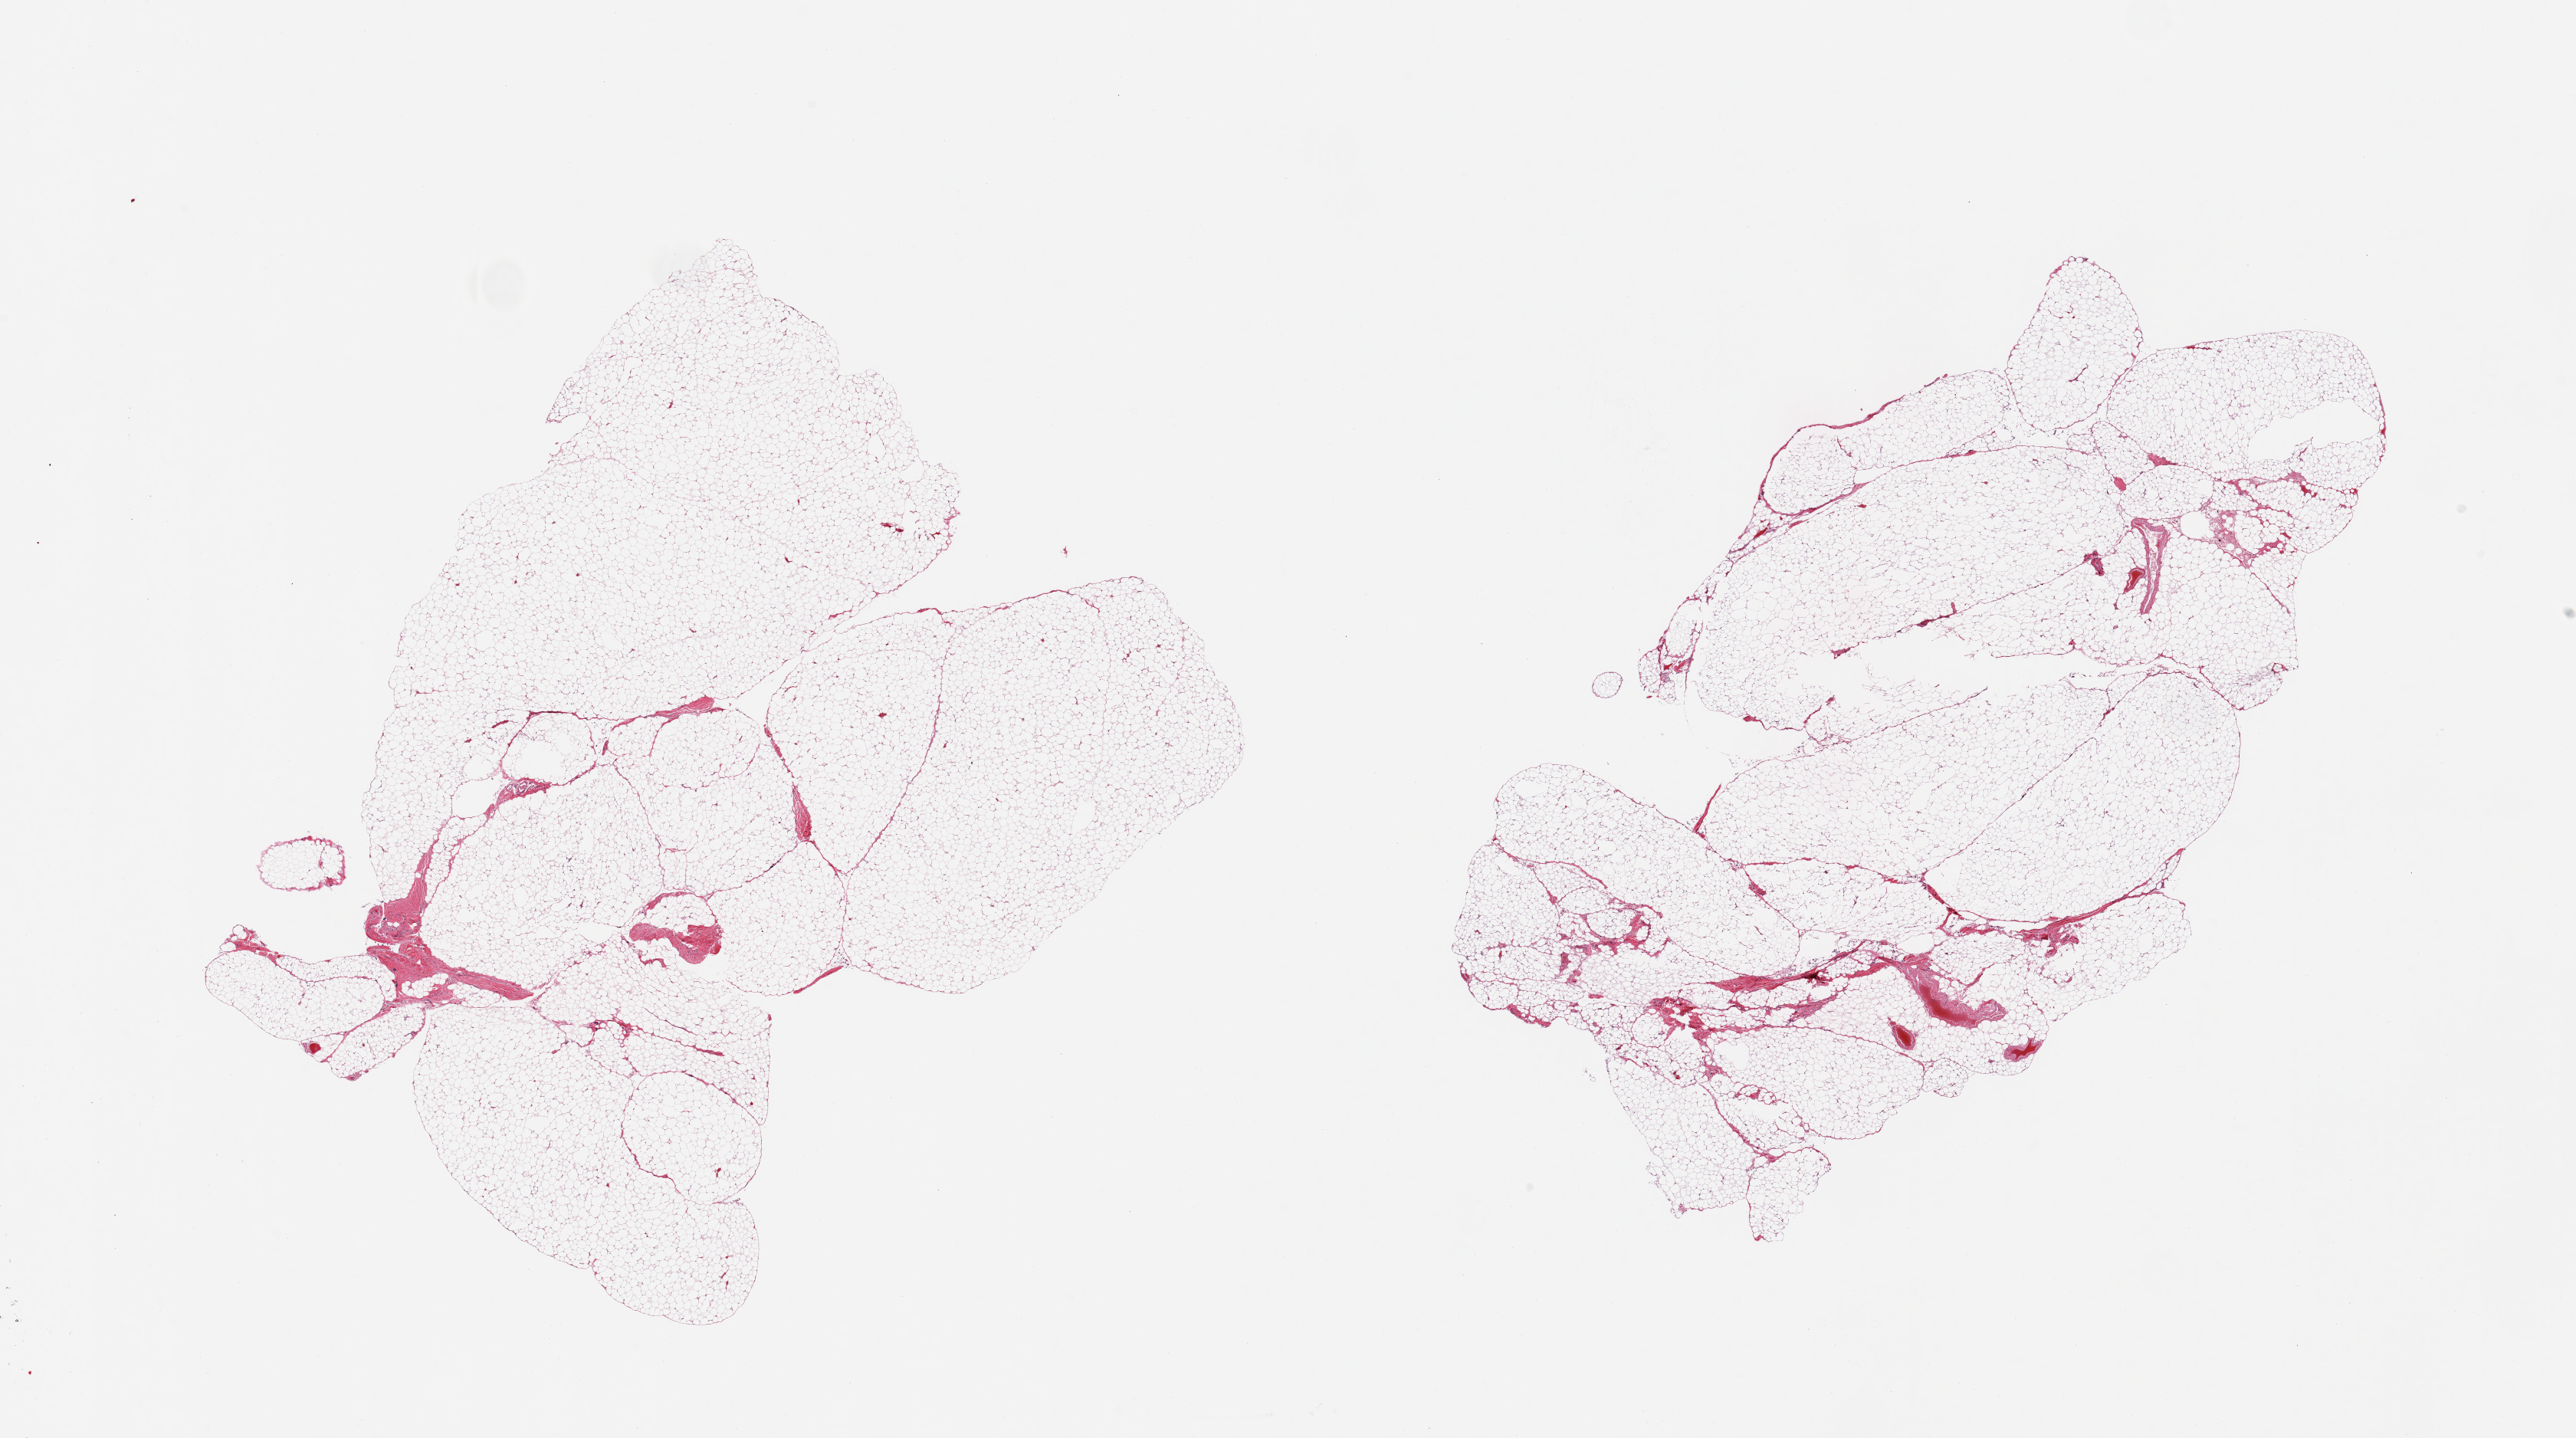
Digitized hematoxylin and eosin (H&E)-stained section, brightfield, low-resolution overview of the scanned area, about 26.6 x 14.8 mm (slide scanned at 20x), PAXgene-fixed, paraffin-embedded tissue, sampled site (target tissue): omentum, tissue donor sample. Donor: female.
Reviewer comment on this tissue sample: 2 pieces; <10% fibrous content.